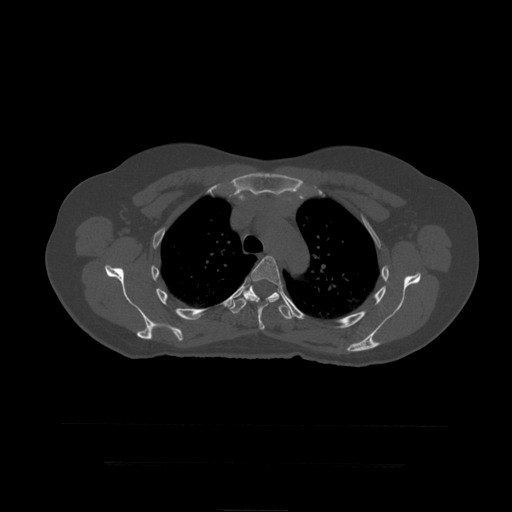
CT including the spine, one axial slice. Position 329 of 399 along the scan axis. 120 kVp. Bone window (W 1800 / L 400 HU). 1.25 mm slice thickness. 512 × 512 image matrix. Patient age 41 years. From the clinical record (not read from this slice): primary cancer: breast.
Annotated regions visible in this slice (semi-automatically segmented with operator editing):
- T5 vertebra: bounding box <243,256,282,330> (left, top, right, bottom; pixels)
- T6 vertebra: <227,285,297,320>